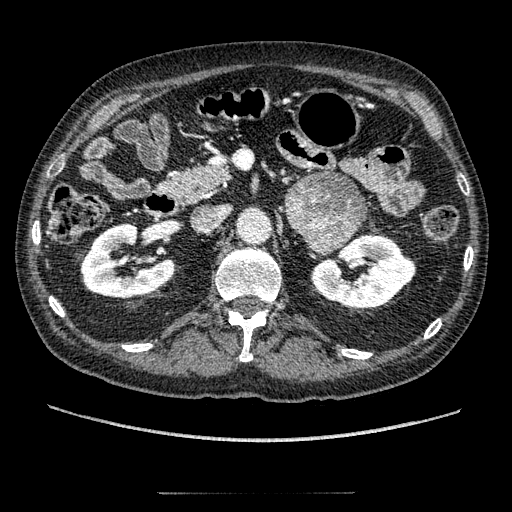
Contrast-enhanced abdominal CT, one axial slice; position 107 of 274 along the scan axis; reconstruction kernel STANDARD; 120 kVp; intravenous contrast given; soft-tissue window (W 400 / L 40 HU); 512 × 512 image matrix, field of view 381 × 381 mm. Patient: male, 69 years. From the clinical record (not read from this slice): diagnosis: adrenocortical carcinoma; tumour side: left adrenal; tumour size at pathology: 6.1 cm; Ki-67 index: 10 %; stage (as recorded): 3.
Annotated regions visible in this slice (semi-automatic segmentation, software-assisted and operator-edited):
- mass: bounding box [x1, y1, x2, y2] px = [286, 172, 367, 253]